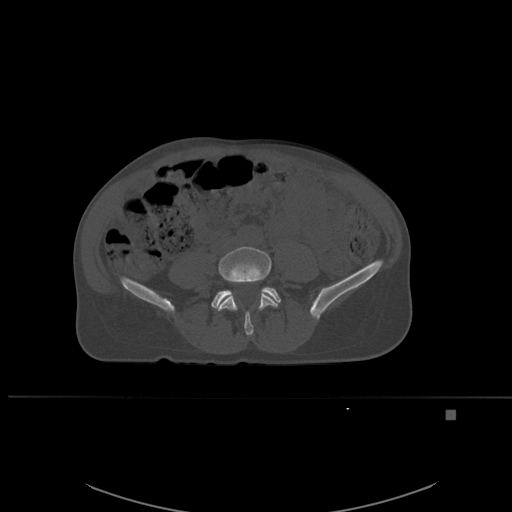
CT including the spine, one axial slice. Slice 184 of 537 in the series (ordered by position). Bone window (W 1800 / L 400 HU). 512 × 512 image matrix. Patient: female, 45 years. Case-level facts recorded for this patient, not image findings: primary cancer: lung.
Outlined on this slice (semi-automatically segmented with operator editing):
- L4 vertebra: bounding box [x1, y1, x2, y2] px = [213, 246, 278, 336]
- L5 vertebra: [212, 287, 281, 308]